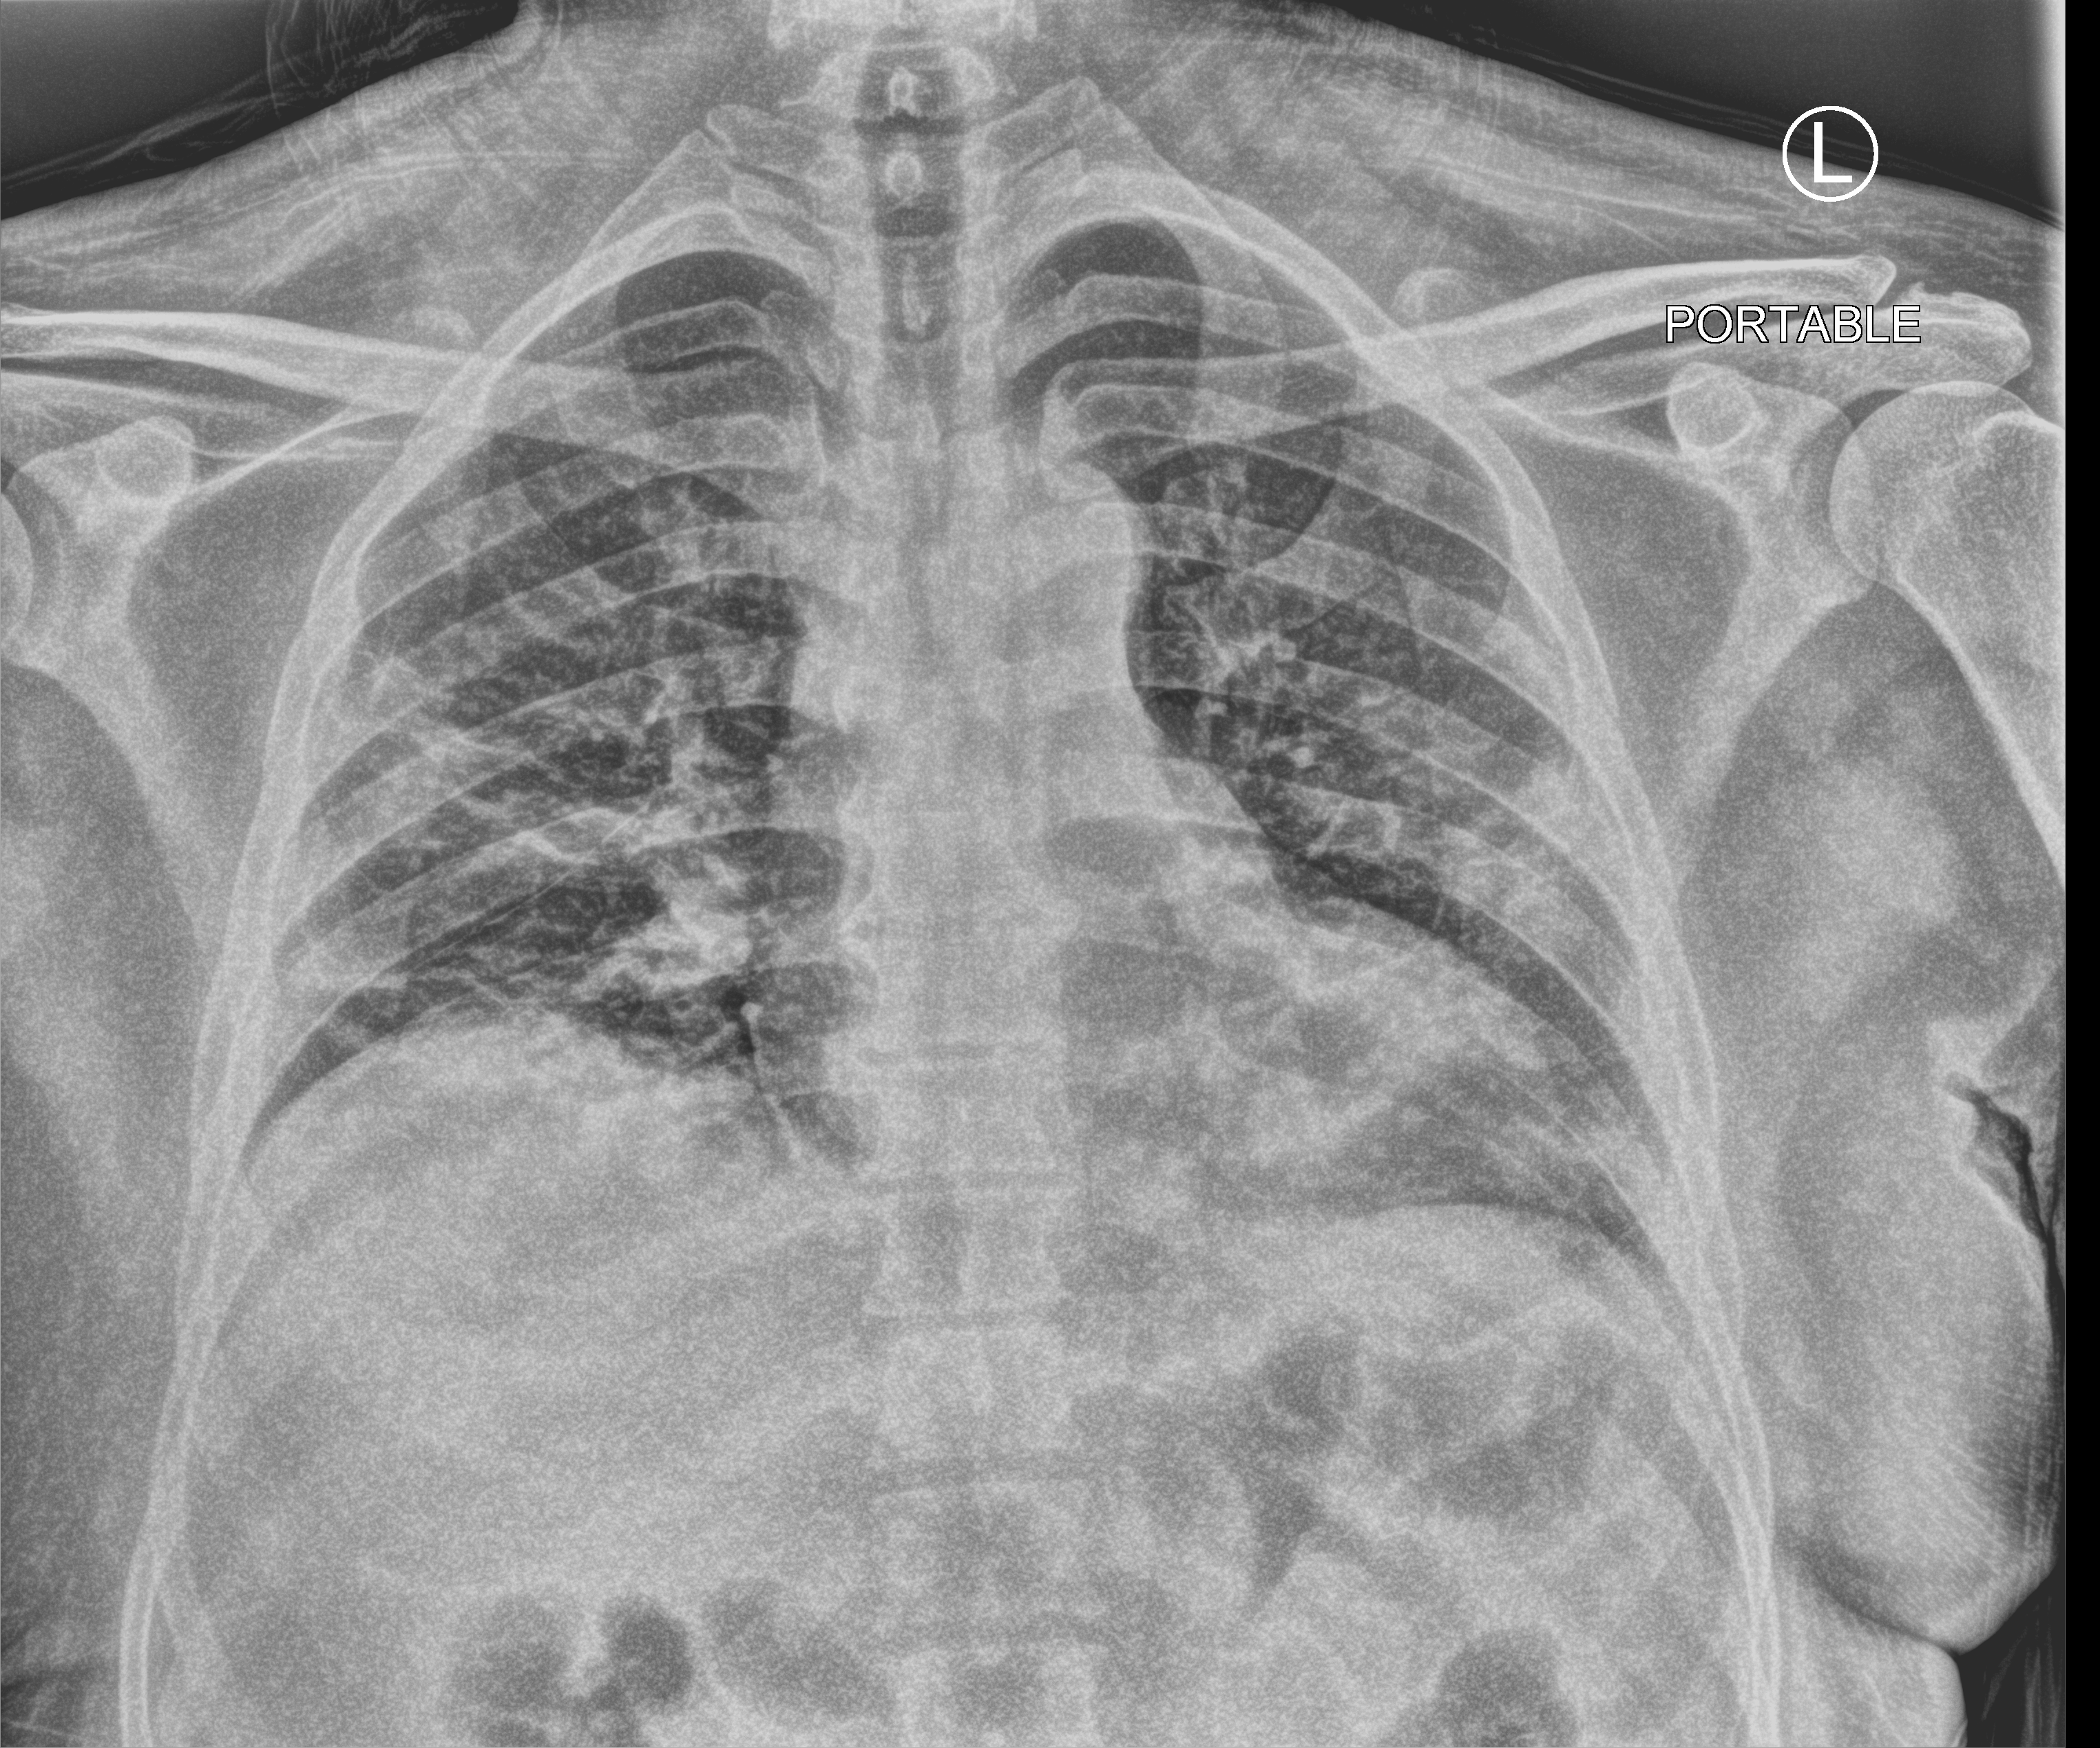
Bedside chest radiograph (computed radiography); anteroposterior (AP) projection. Male patient hospitalised with COVID-19, age 18–59 years.
Admission-level facts for this patient (not findings on this image; timing relative to this image not recorded): admitted to intensive care during this hospital stay: no; length of hospital stay: 4 days.